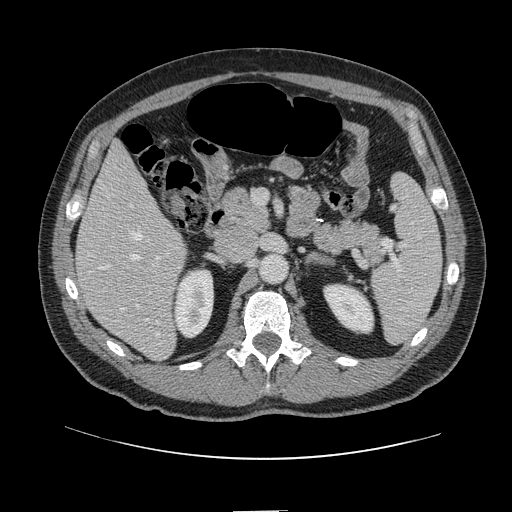
Contrast-enhanced abdominal CT, one axial slice; position 59 of 161 along the scan axis; soft-tissue window (W 400 / L 40 HU); 2.5 mm slice thickness; 512 × 512 image matrix, field of view 412 × 412 mm. Male patient, age 66 years. From the clinical record (not read from this slice): diagnosis: colorectal cancer liver metastases, imaged before liver resection; multiple liver metastases: no; largest metastasis: 3.5 cm; disease in both lobes: no.
Annotated regions visible in this slice (outlined manually by an expert reader):
- hepatic veins: bounding box [x1, y1, x2, y2] px = [122, 232, 159, 336]
- liver: [77, 144, 186, 360]
- planned liver remnant (the part of the liver to remain after resection): [77, 144, 170, 283]
- portal vein (with intrahepatic branches): [148, 255, 161, 295]